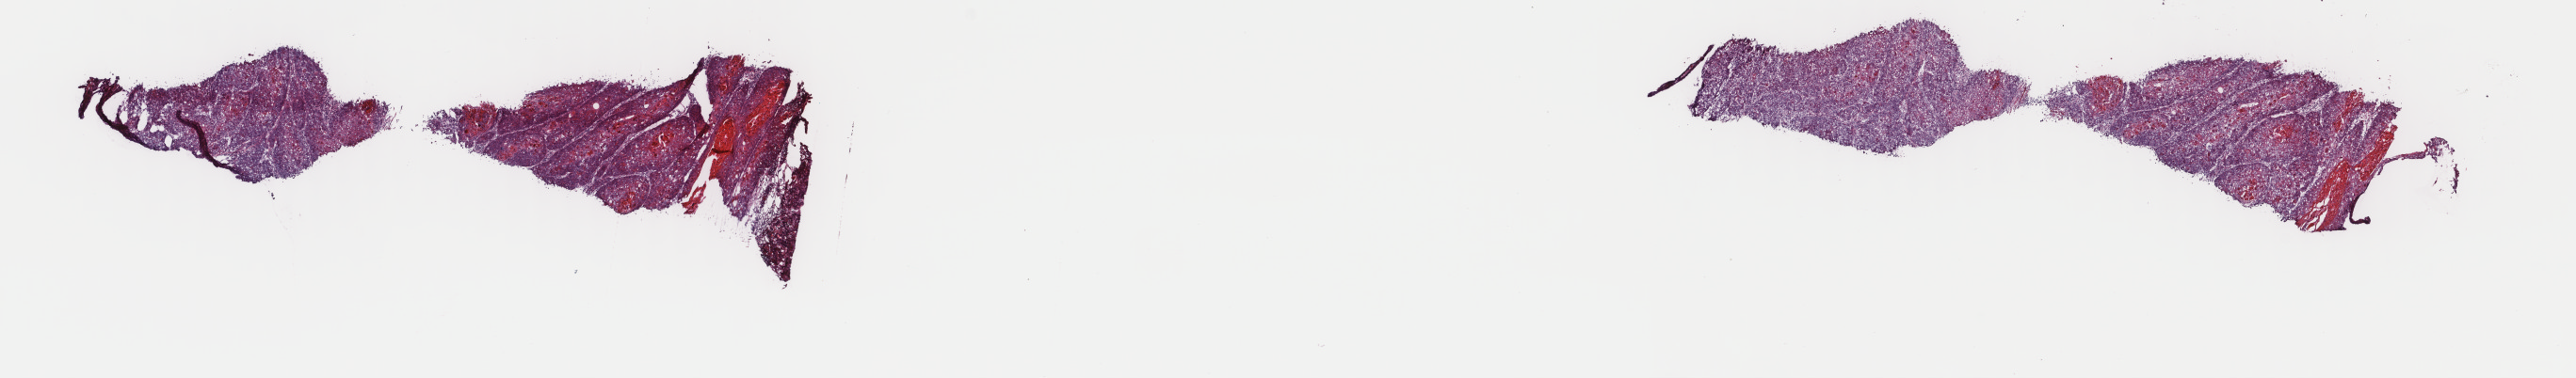
Whole-slide histology image, H&E — a low-resolution overview of the entire scanned area, about 21.7 x 3.2 mm; frozen section from the top of the tissue portion; sample: primary tumour, head and neck. Male, age 59 years at initial diagnosis. Pathologist review of this section (percent, as recorded): tumour cells 95%, tumour nuclei 95%.
Pathologic diagnosis: Squamous cell carcinoma, keratinizing, NOS.